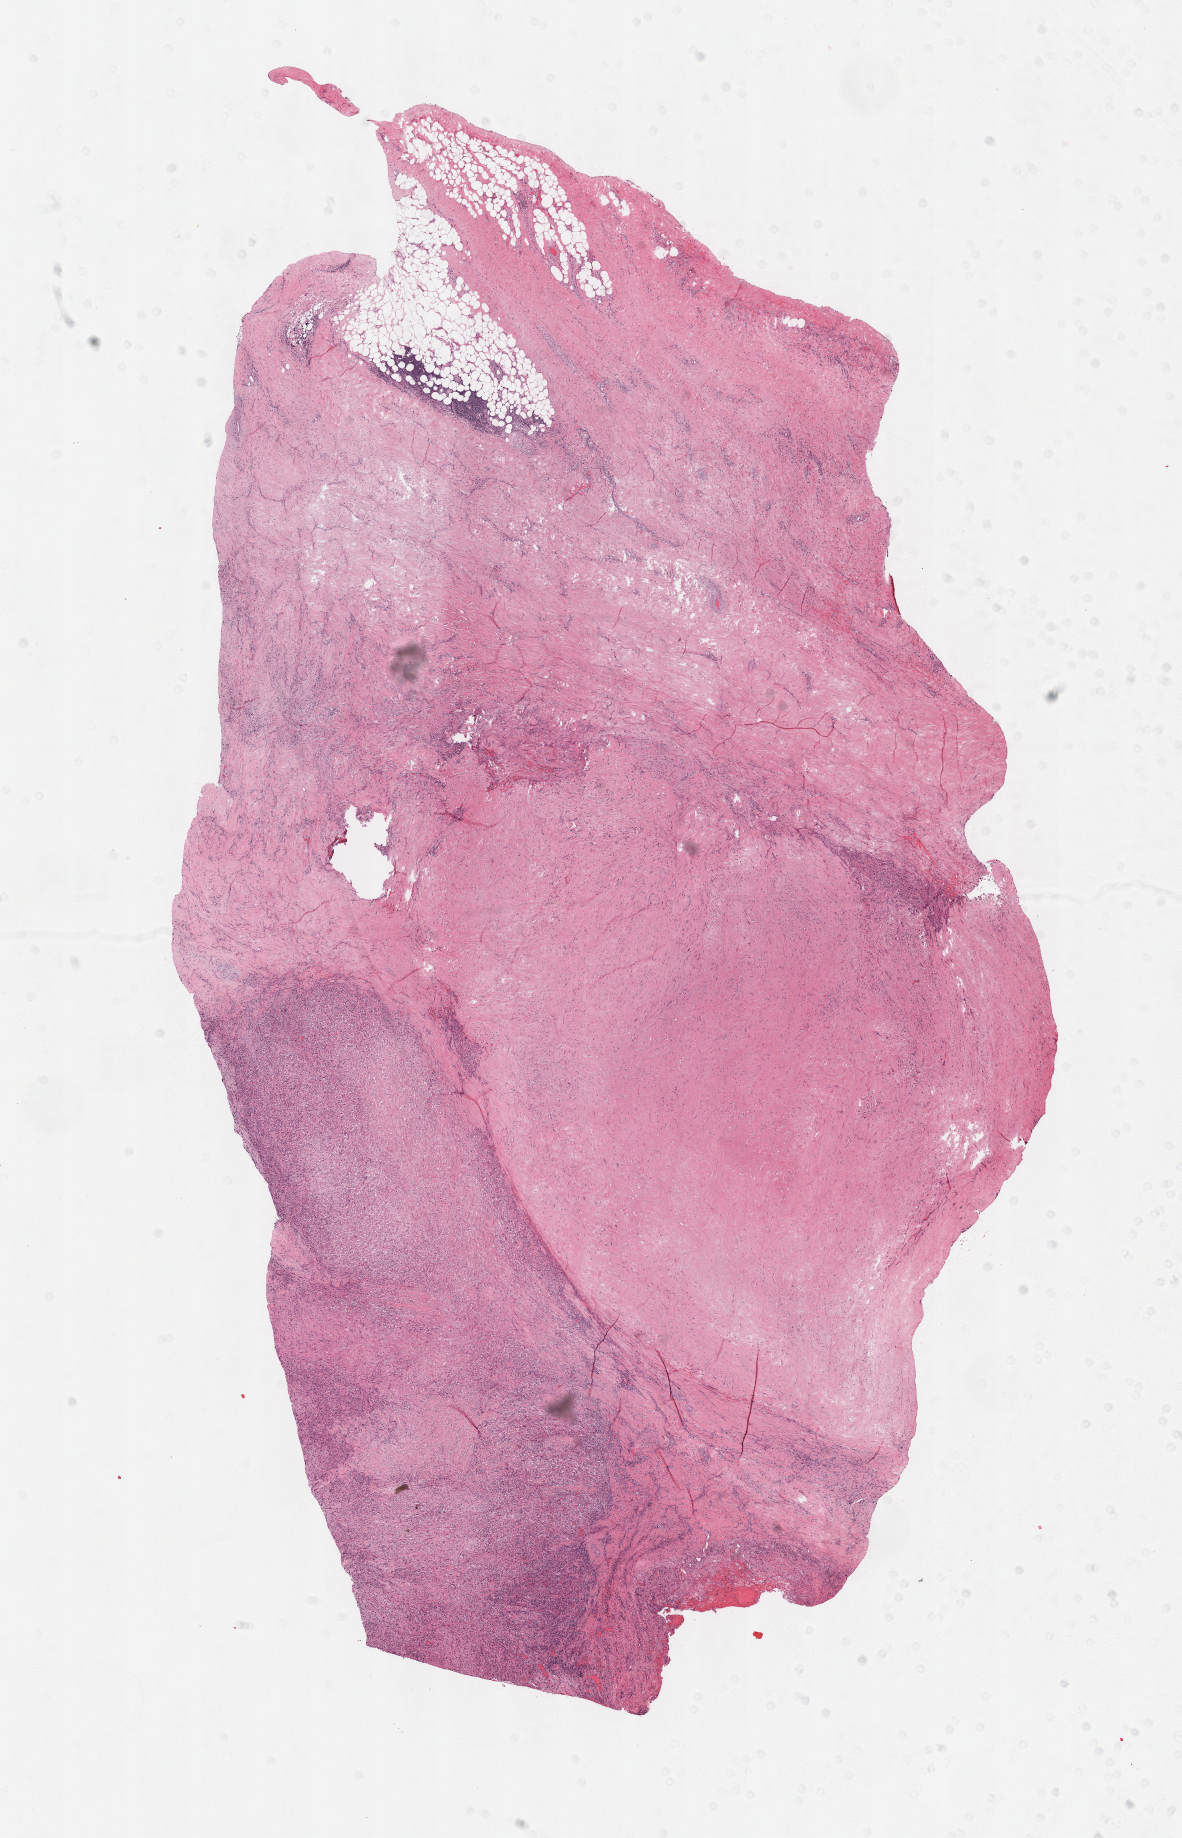
Whole-slide histology image, H&E — a low-resolution overview of the entire scanned area, about 9.6 x 14.9 mm, formalin-fixed paraffin-embedded (FFPE) diagnostic section, mesothelium, primary tumour sample. Male, age 55 years at initial diagnosis.
AJCC pathologic stage: III (6th edition). Pathologic diagnosis: Fibrous mesothelioma, malignant (pleura, NOS).